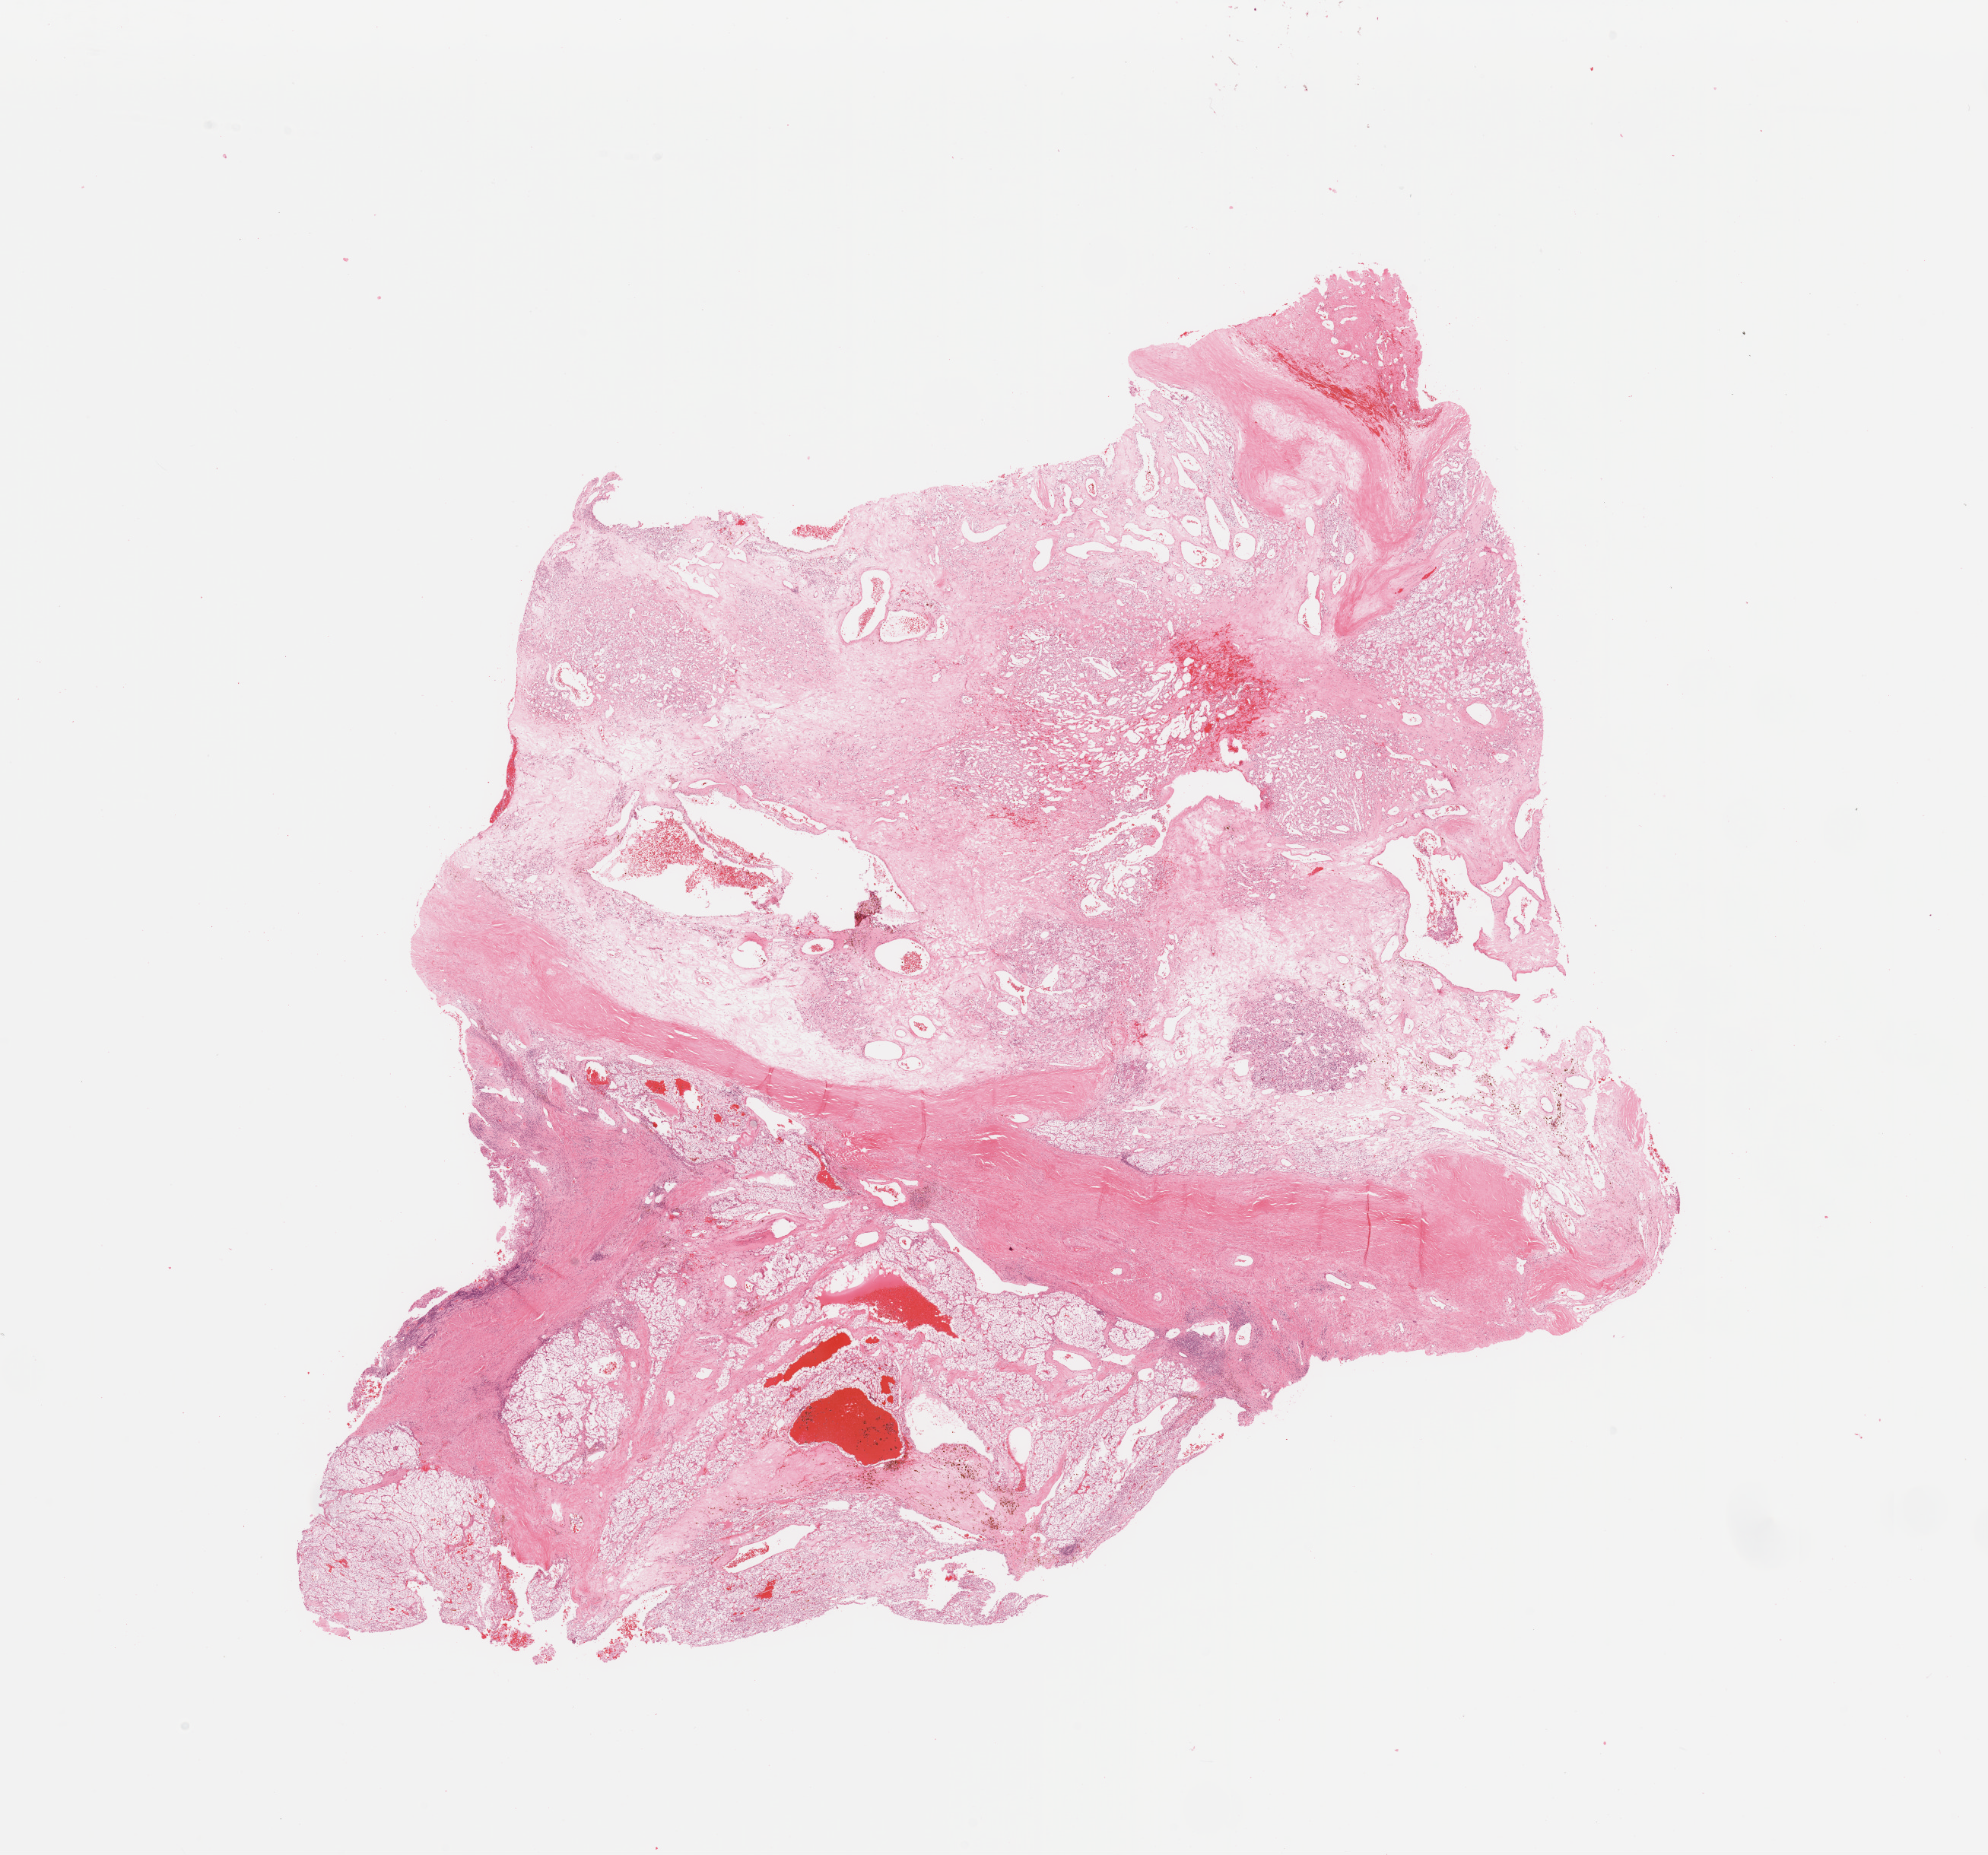
Whole-slide histology image, H&E — low-resolution overview of the scanned area, about 20.7 x 19.3 mm (slide scanned at 20x); tumour tissue sample, kidney. Patient: male, age 66 years. Histologic grade: G1 (well differentiated).
Diagnosis: Renal cell carcinoma, NOS.